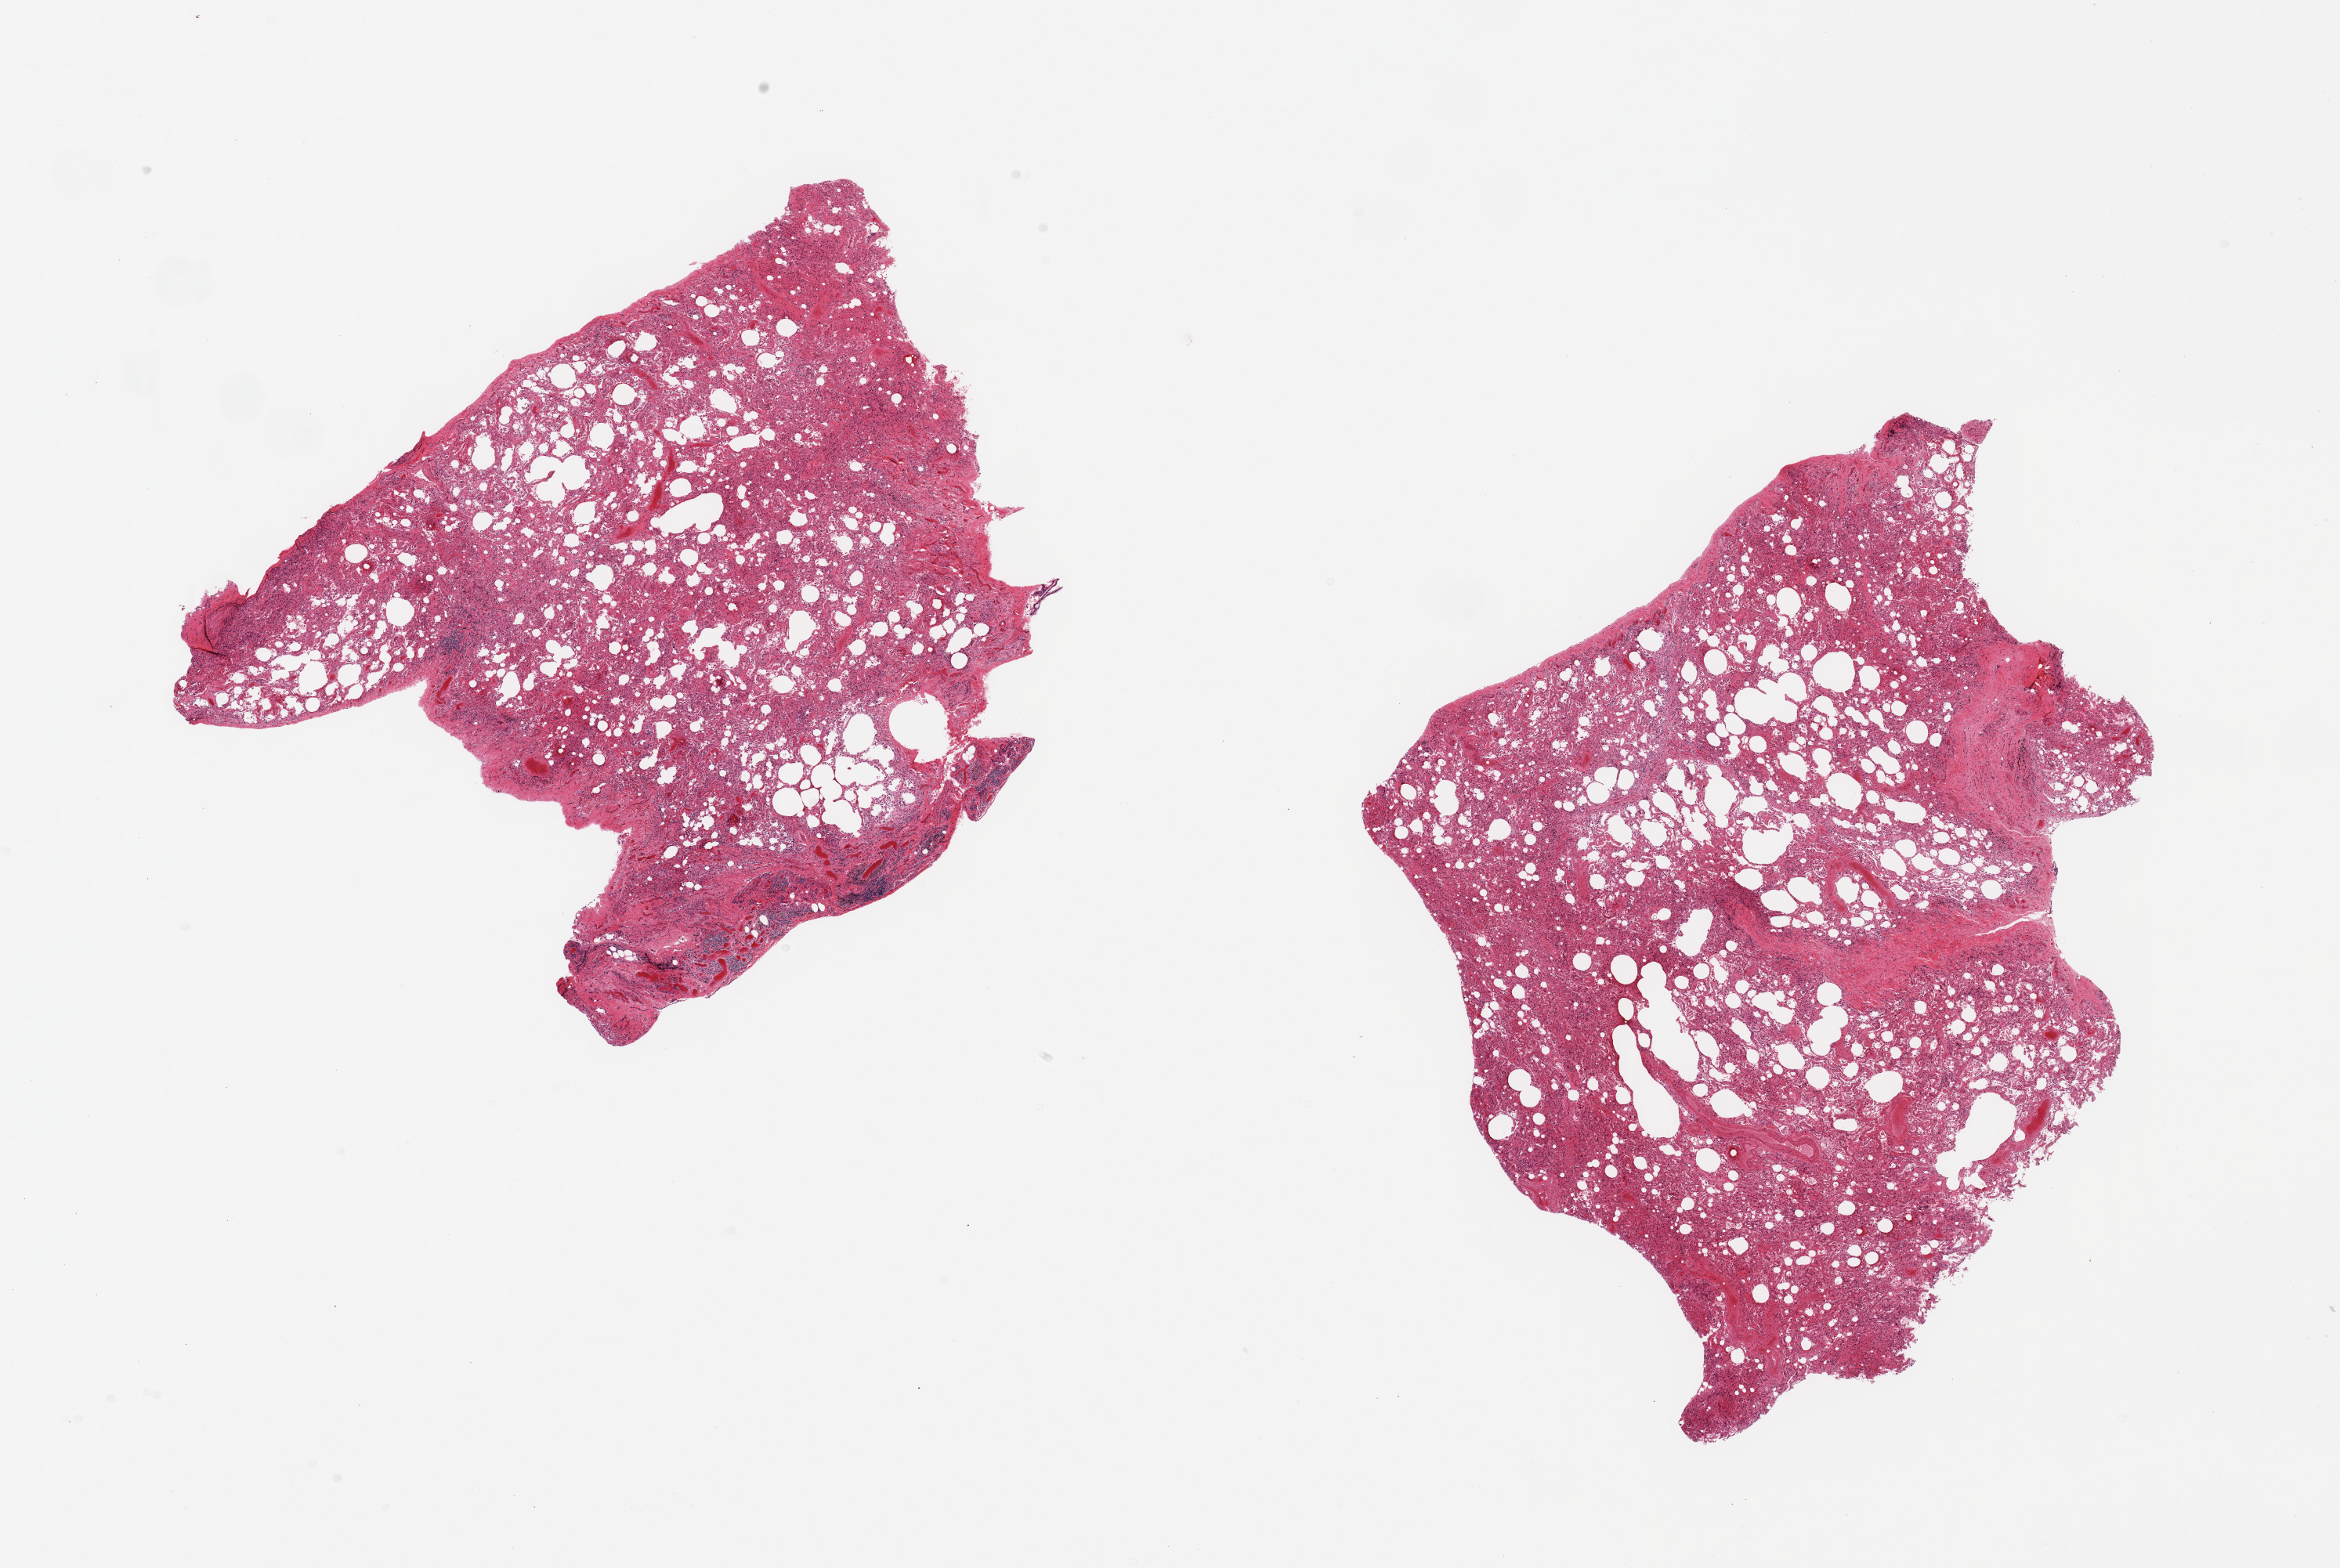
Digitized hematoxylin and eosin (H&E)-stained section, brightfield, low-resolution overview of the scanned area, about 23.6 x 15.8 mm; PAXgene-fixed, paraffin-embedded tissue; sampled site (target tissue): lung; tissue donor sample.
Review note (as recorded): 2 pieces; emphysema, atelectasis, numerous alveolar macrophages; pleura sampled.